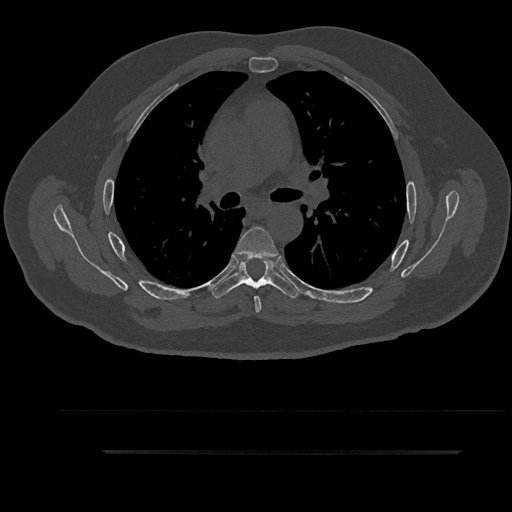
CT including the spine, one axial slice. Position 601 of 797 along the scan axis. Reconstruction kernel Br40s/3. 120 kVp. Bone window (W 1800 / L 400 HU). 0.5 mm slice thickness. 512 × 512 image matrix, field of view 432 × 432 mm. Patient: male, 63 years. Case-level facts recorded for this patient, not image findings: primary cancer: renal.
Outlined on this slice (semi-automatic segmentation, software-assisted and operator-edited):
- T5 vertebra: box from (x=234, y=226) to (x=280, y=313) px
- T6 vertebra: (x=211, y=257)–(x=300, y=298)